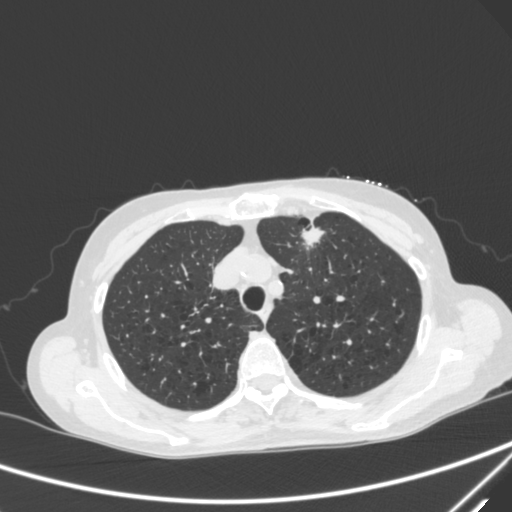
Chest CT, one axial slice; slice 234 of 300 in the series (ordered by position); 120 kVp; lung window (W 1500 / L -600 HU); 1 mm slice thickness; 512 × 512 image matrix, field of view 350 × 350 mm. Female patient, age 71 years. From the clinical record (not read from this slice): clinical TNM (as recorded): T1c N0 M0.
Outlined on this slice (bounding box drawn by a radiologist):
- lung tumour (recorded histology: adenocarcinoma): bounding box [x1, y1, x2, y2] px = [292, 215, 329, 253]